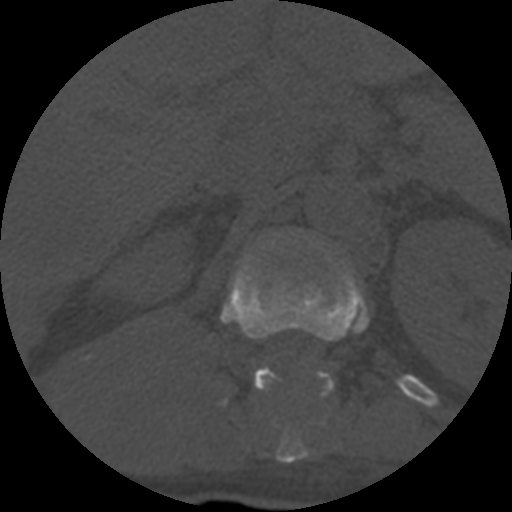
CT including the spine, one axial slice. Slice 305 of 708 in the series (ordered by position). 120 kVp. One of 3 acquisitions stored at this slice position. Bone window (W 1800 / L 400 HU). 1.25 mm slice thickness. 512 × 512 image matrix, field of view 160 × 160 mm. Patient age 55 years. Case-level facts recorded for this patient, not image findings: primary cancer: colon.
Outlined on this slice (semi-automatic segmentation, software-assisted and operator-edited):
- T12 vertebra: bounding box <221,239,369,463> (left, top, right, bottom; pixels)